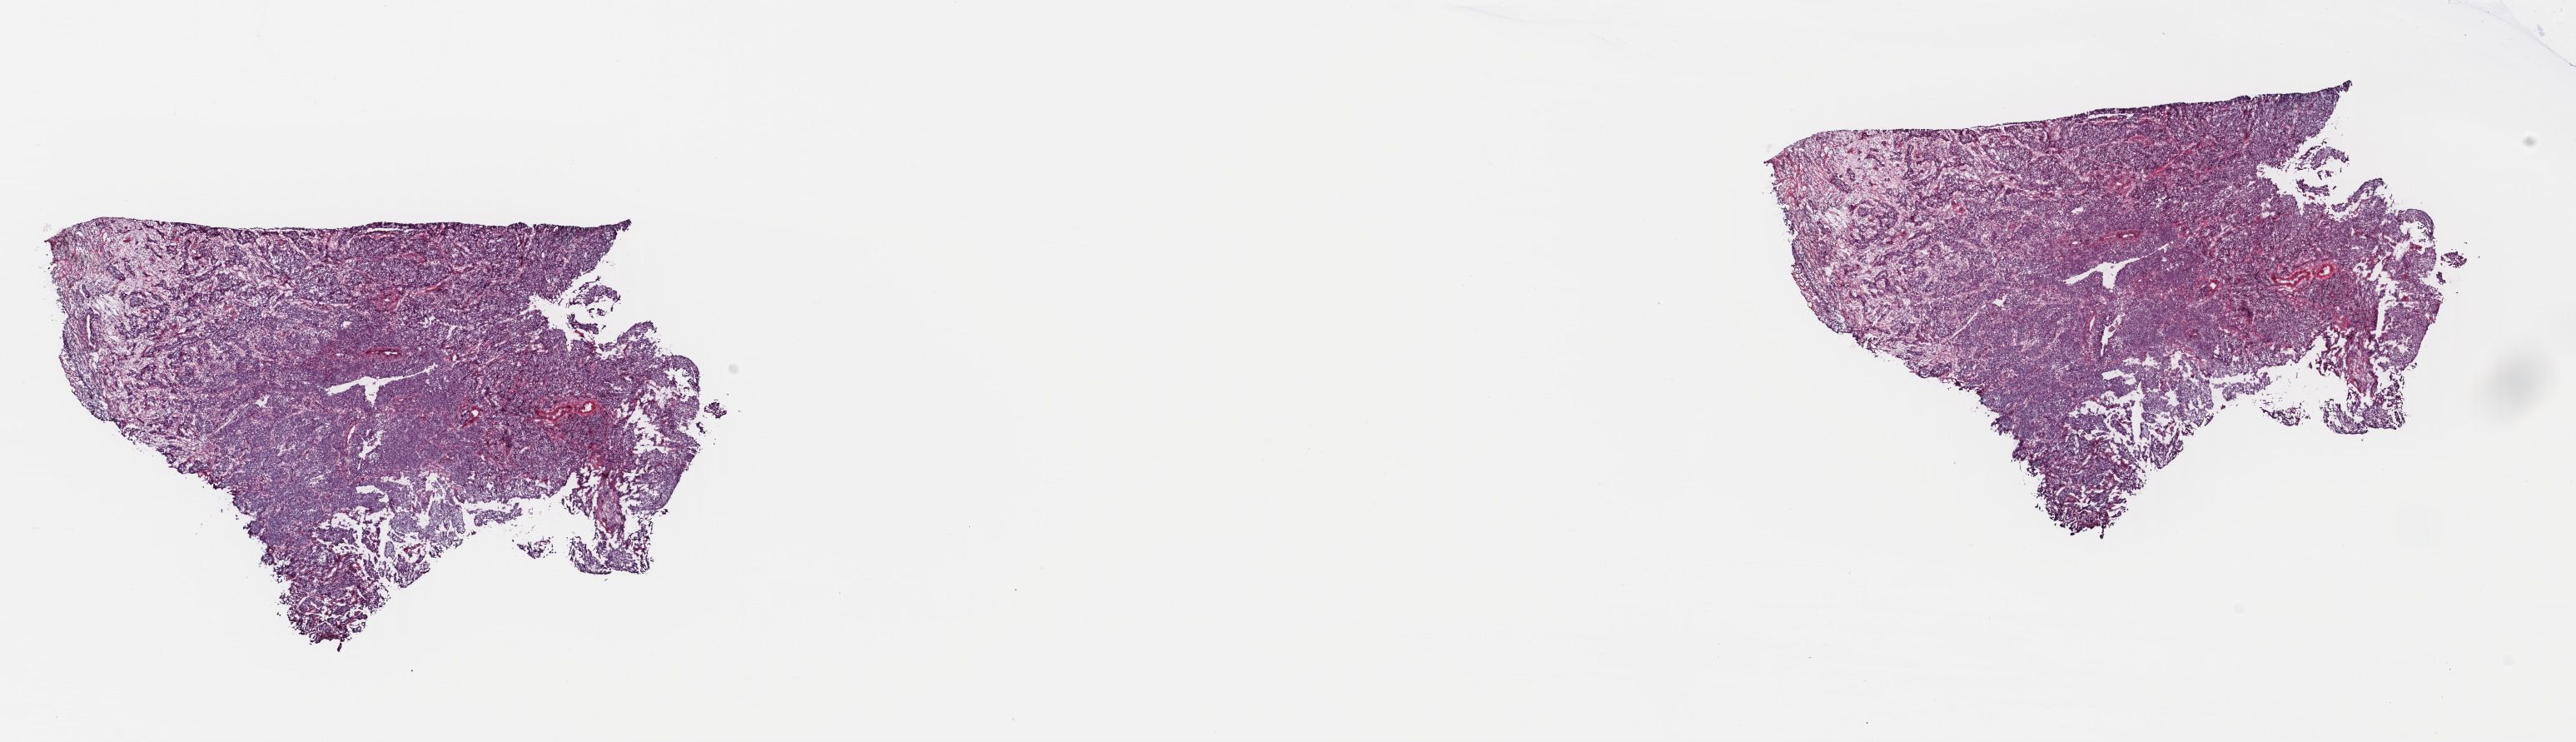
Hematoxylin and eosin (H&E) stained whole-slide image — shown as a low-resolution overview of the whole scanned area (about 24.3 x 7.0 mm). Frozen section. Cervix, primary tumour sample. Female, age 56 years at initial diagnosis.
Diagnosis: Squamous cell carcinoma, NOS (cervix uteri).